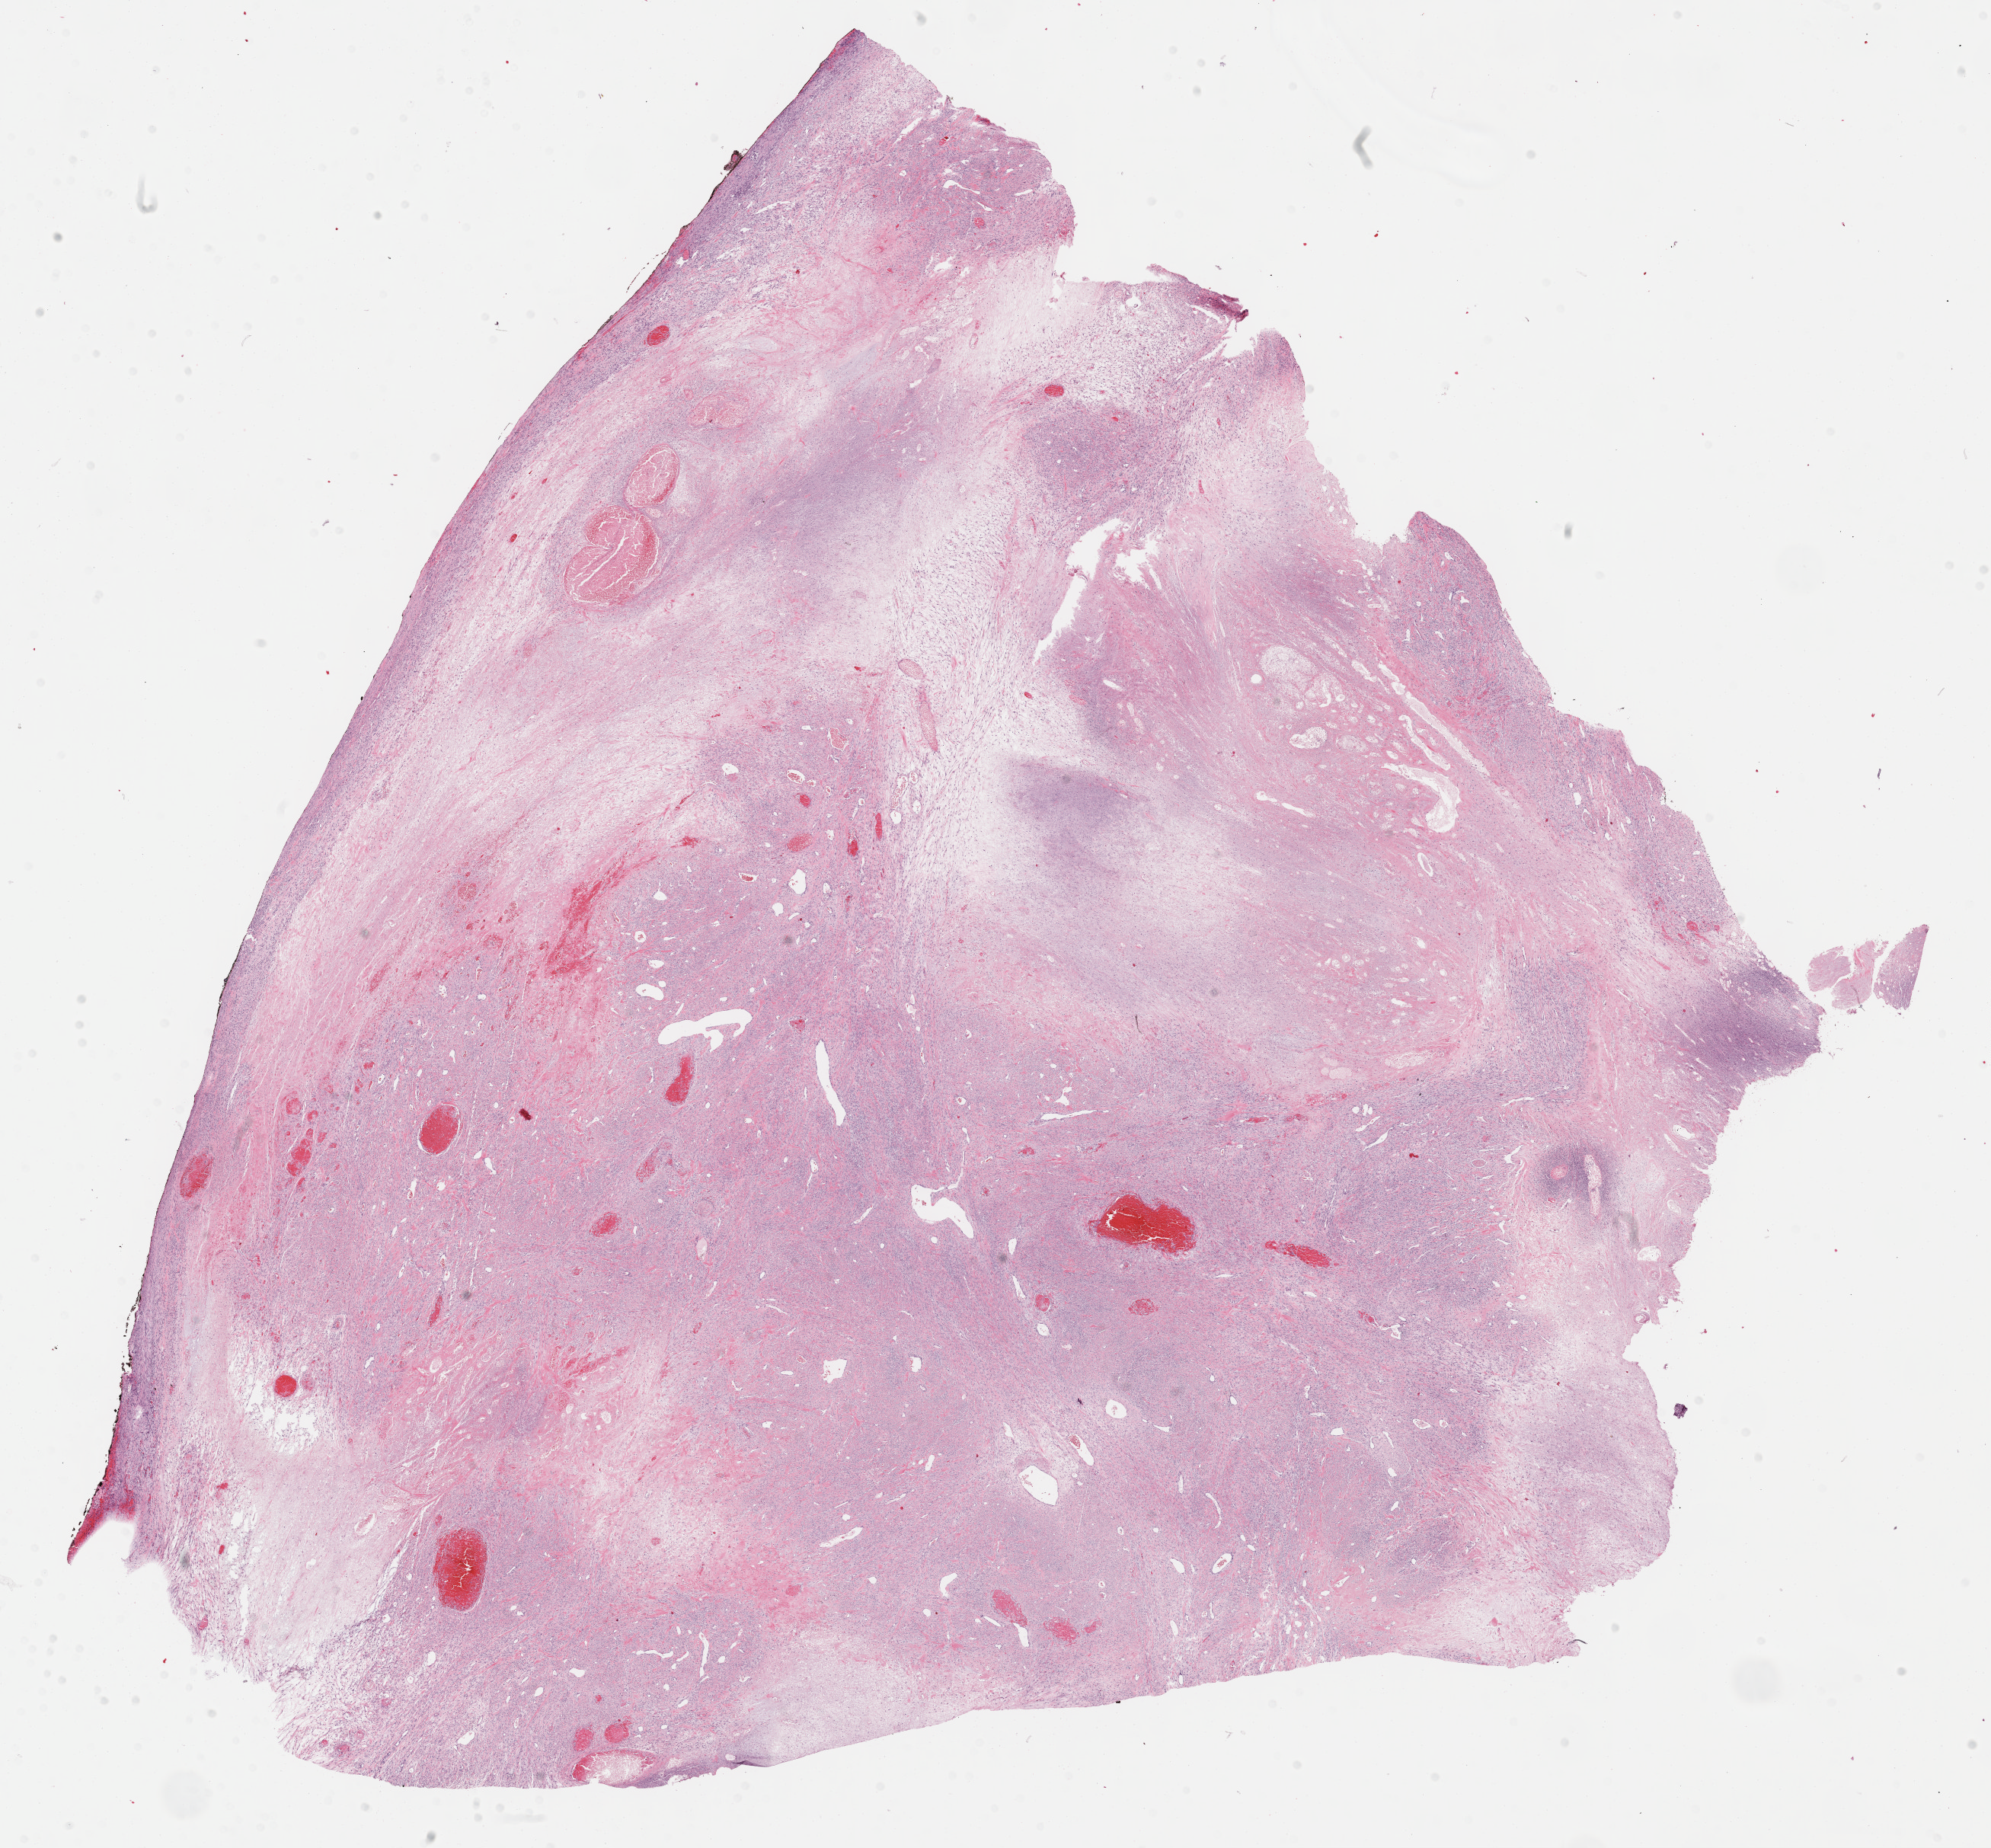
Whole-slide histology image, Hematoxylin and eosin (H&E) stained — shown as a low-resolution overview of the whole scanned area (about 21.1 x 19.6 mm, slide scanned at 40x); formalin-fixed paraffin-embedded (FFPE) diagnostic section; sample: primary tumour, retroperitoneum and peritoneum. Female, age 71 years at initial diagnosis.
Histologic diagnosis: Undifferentiated sarcoma (retroperitoneum).